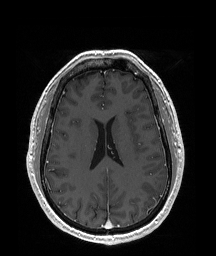
Brain MRI from a brain-tumour surgery series, one axial slice; slice 82 of 192 in the series (ordered by position); T1-weighted post-contrast; 1 mm slice thickness; 216 × 256 image matrix, field of view 219 × 260 mm. From the clinical record (not read from this slice): histopathology: Glioblastoma; WHO grade: 4; IDH mutation: no.
Outlined on this slice (manually delineated by an expert):
- tumour: bounding box <142,181,163,208> (left, top, right, bottom; pixels)